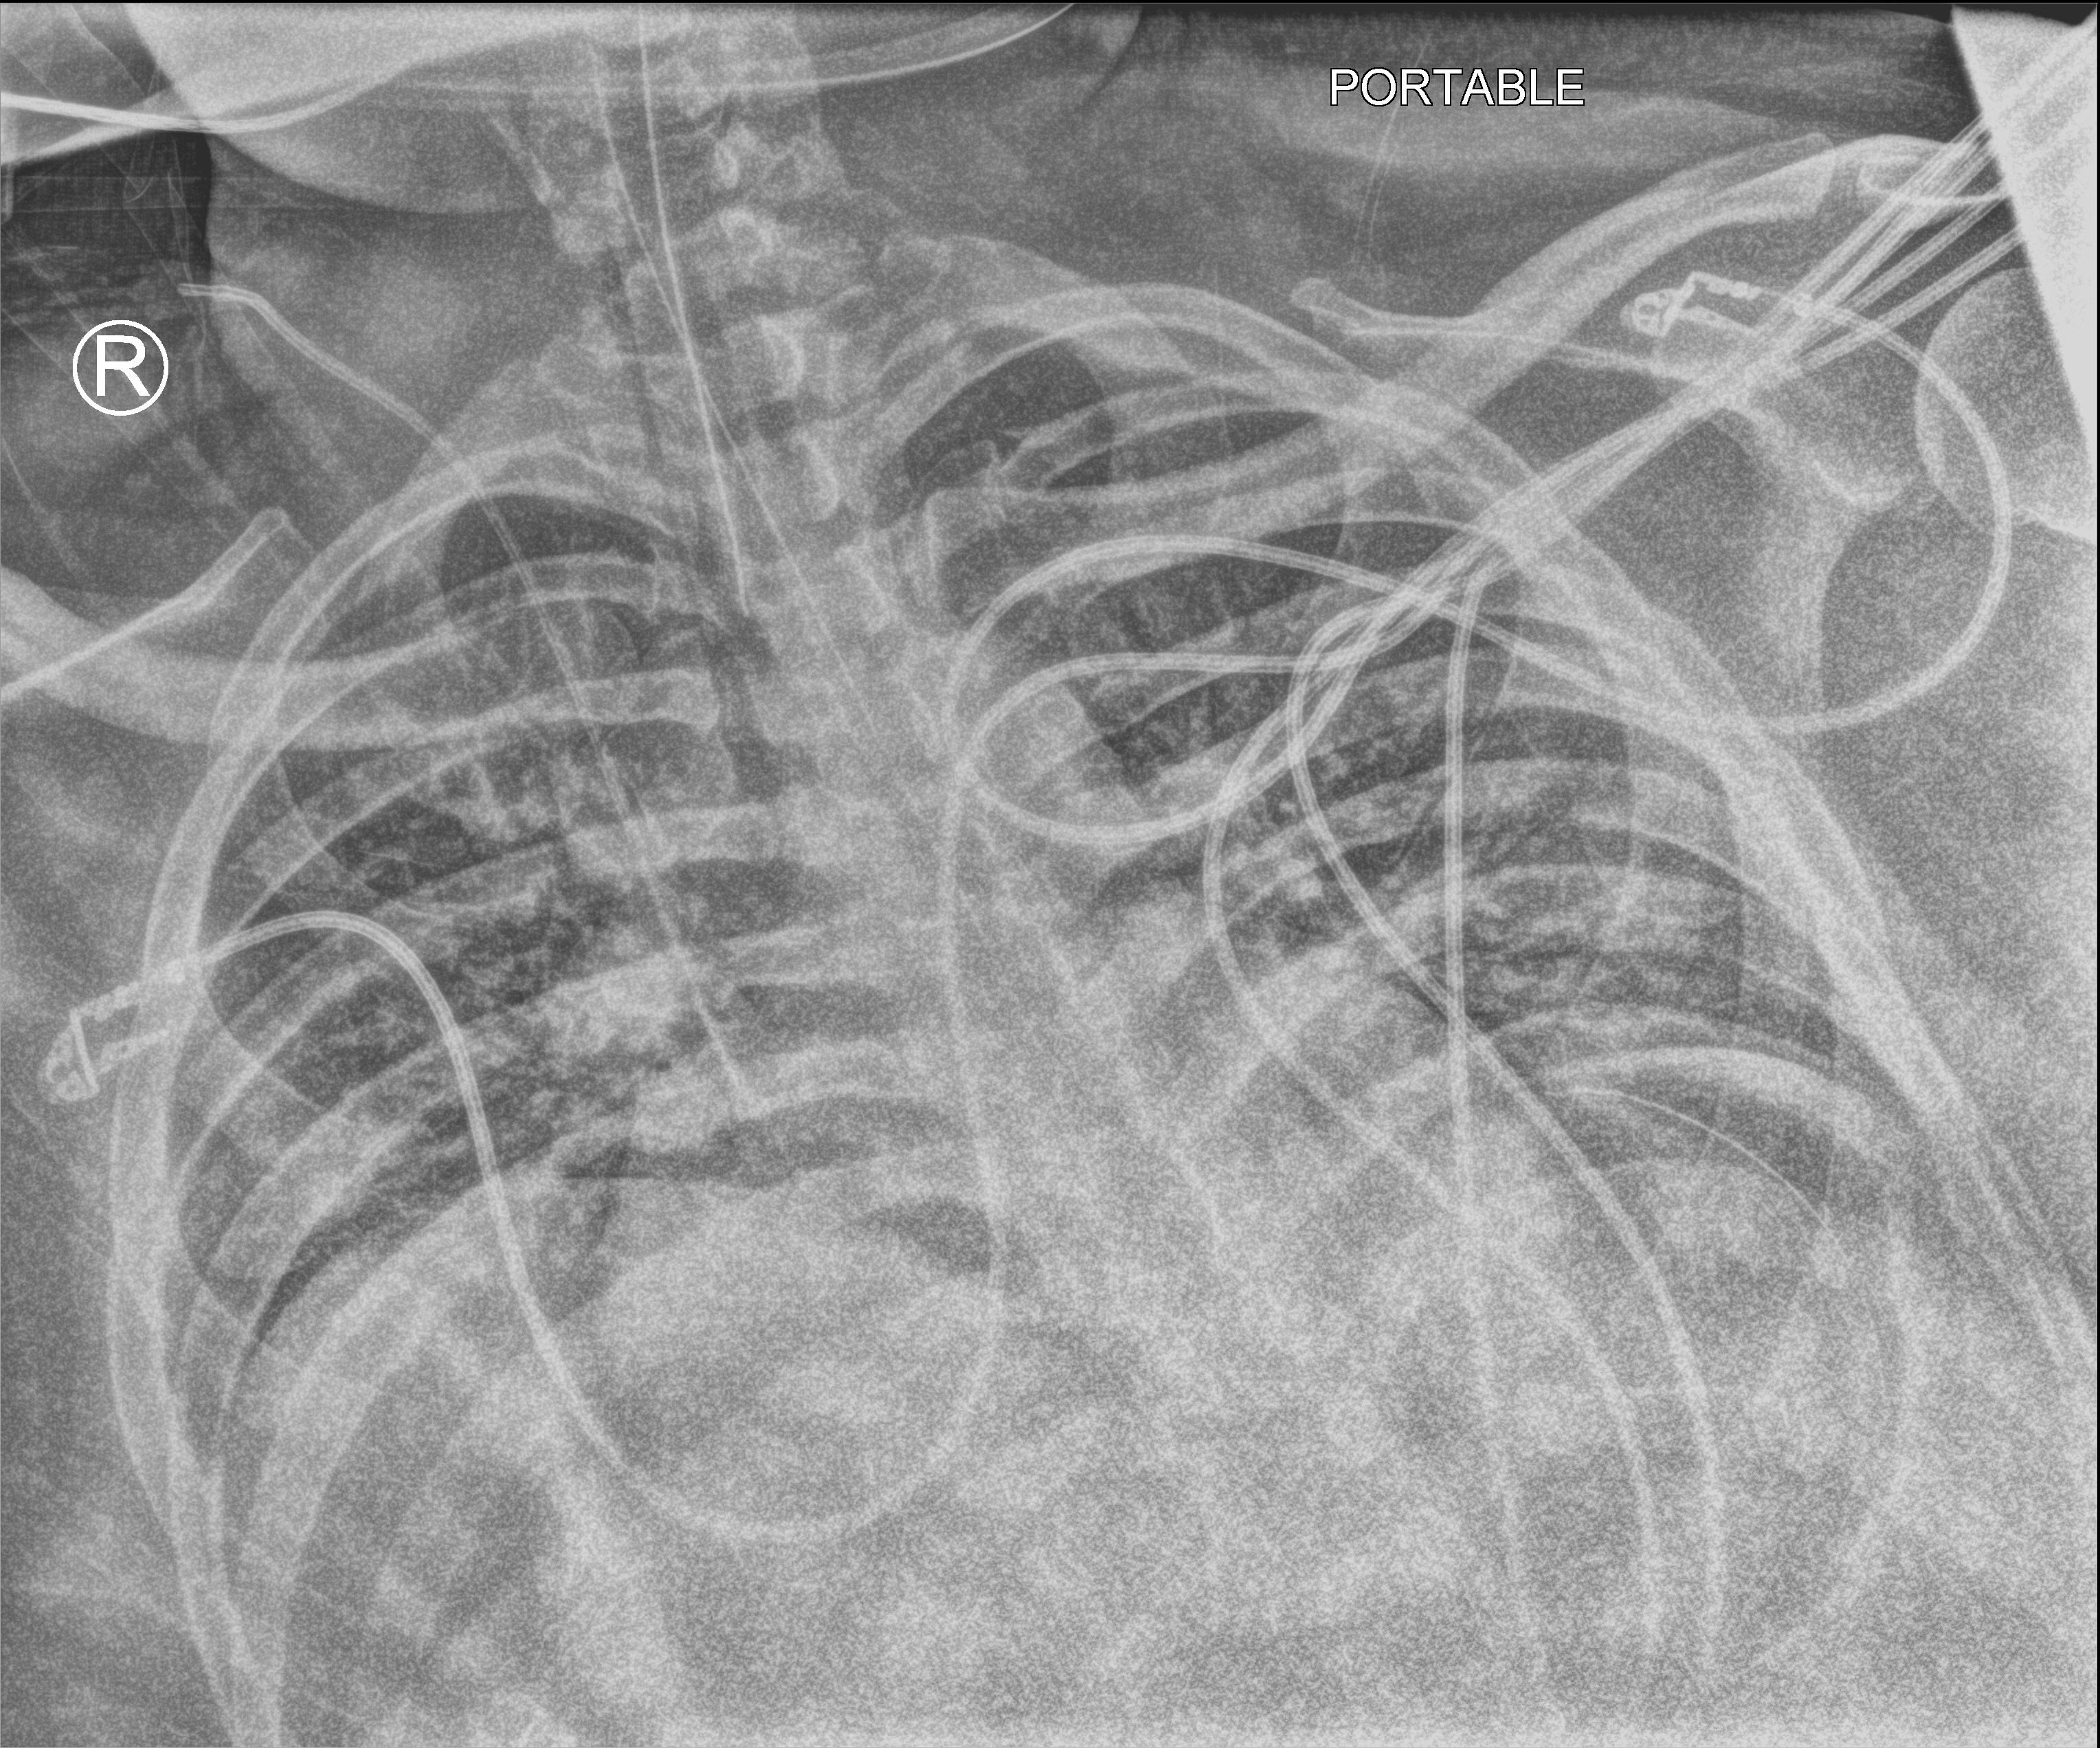
Bedside chest radiograph (computed radiography), anteroposterior (AP) projection. Male patient hospitalised with COVID-19, age 18–59 years.
Admission-level facts for this patient (not findings on this image; timing relative to this image not recorded):
- admitted to intensive care during this hospital stay: yes
- mechanically ventilated during this hospital stay: yes